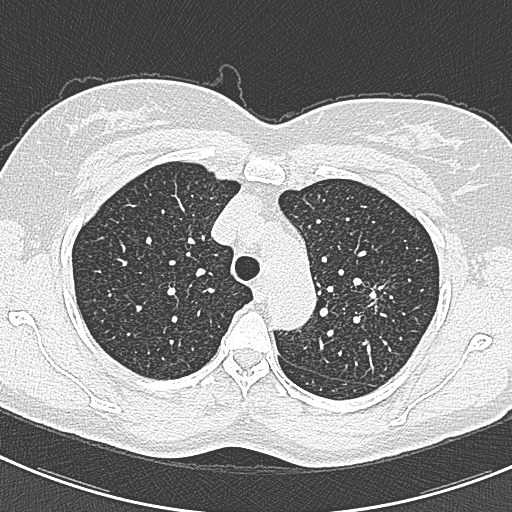
Chest CT (low-dose screening protocol), one axial image; first (baseline) screen; lung window (W 1500 / L -600 HU); lung (sharp) reconstruction kernel (B80f). Female, age 57 years at enrolment.
Lesion marked by an expert reader, box from (x=362, y=269) to (x=412, y=324) px. The screening reader recorded 2 non-calcified nodules or masses ≥4 mm on this exam; which of them this box marks is not recorded. Lung cancer was diagnosed 198 days after this screen: adenocarcinoma, NOS, left upper lobe, well differentiated (G1), stage IA (AJCC 6th edition), 10 mm at pathology.